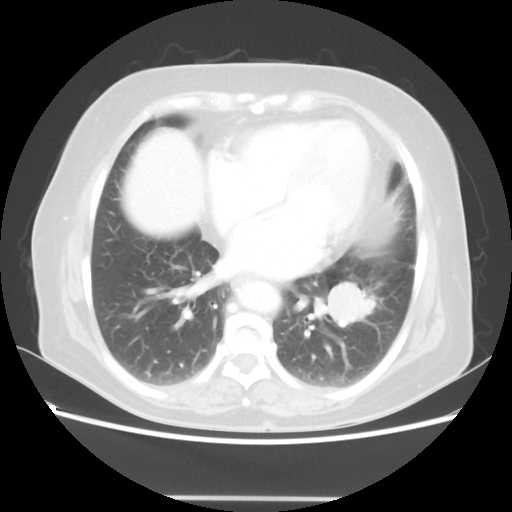
Chest CT, one axial slice. Slice 23 of 56 in the series (ordered by position). Reconstruction kernel STANDARD. 100 kVp. Lung window (W 1500 / L -600 HU). 512 × 512 image matrix, field of view 360 × 360 mm. Female patient, age 73 years. Case-level facts recorded for this patient, not image findings: clinical TNM (as recorded): T1c N0 M0.
Annotated regions visible in this slice (rectangle marked by the reading radiologist):
- lung tumour (recorded histology: adenocarcinoma): box from (x=321, y=276) to (x=381, y=335) px